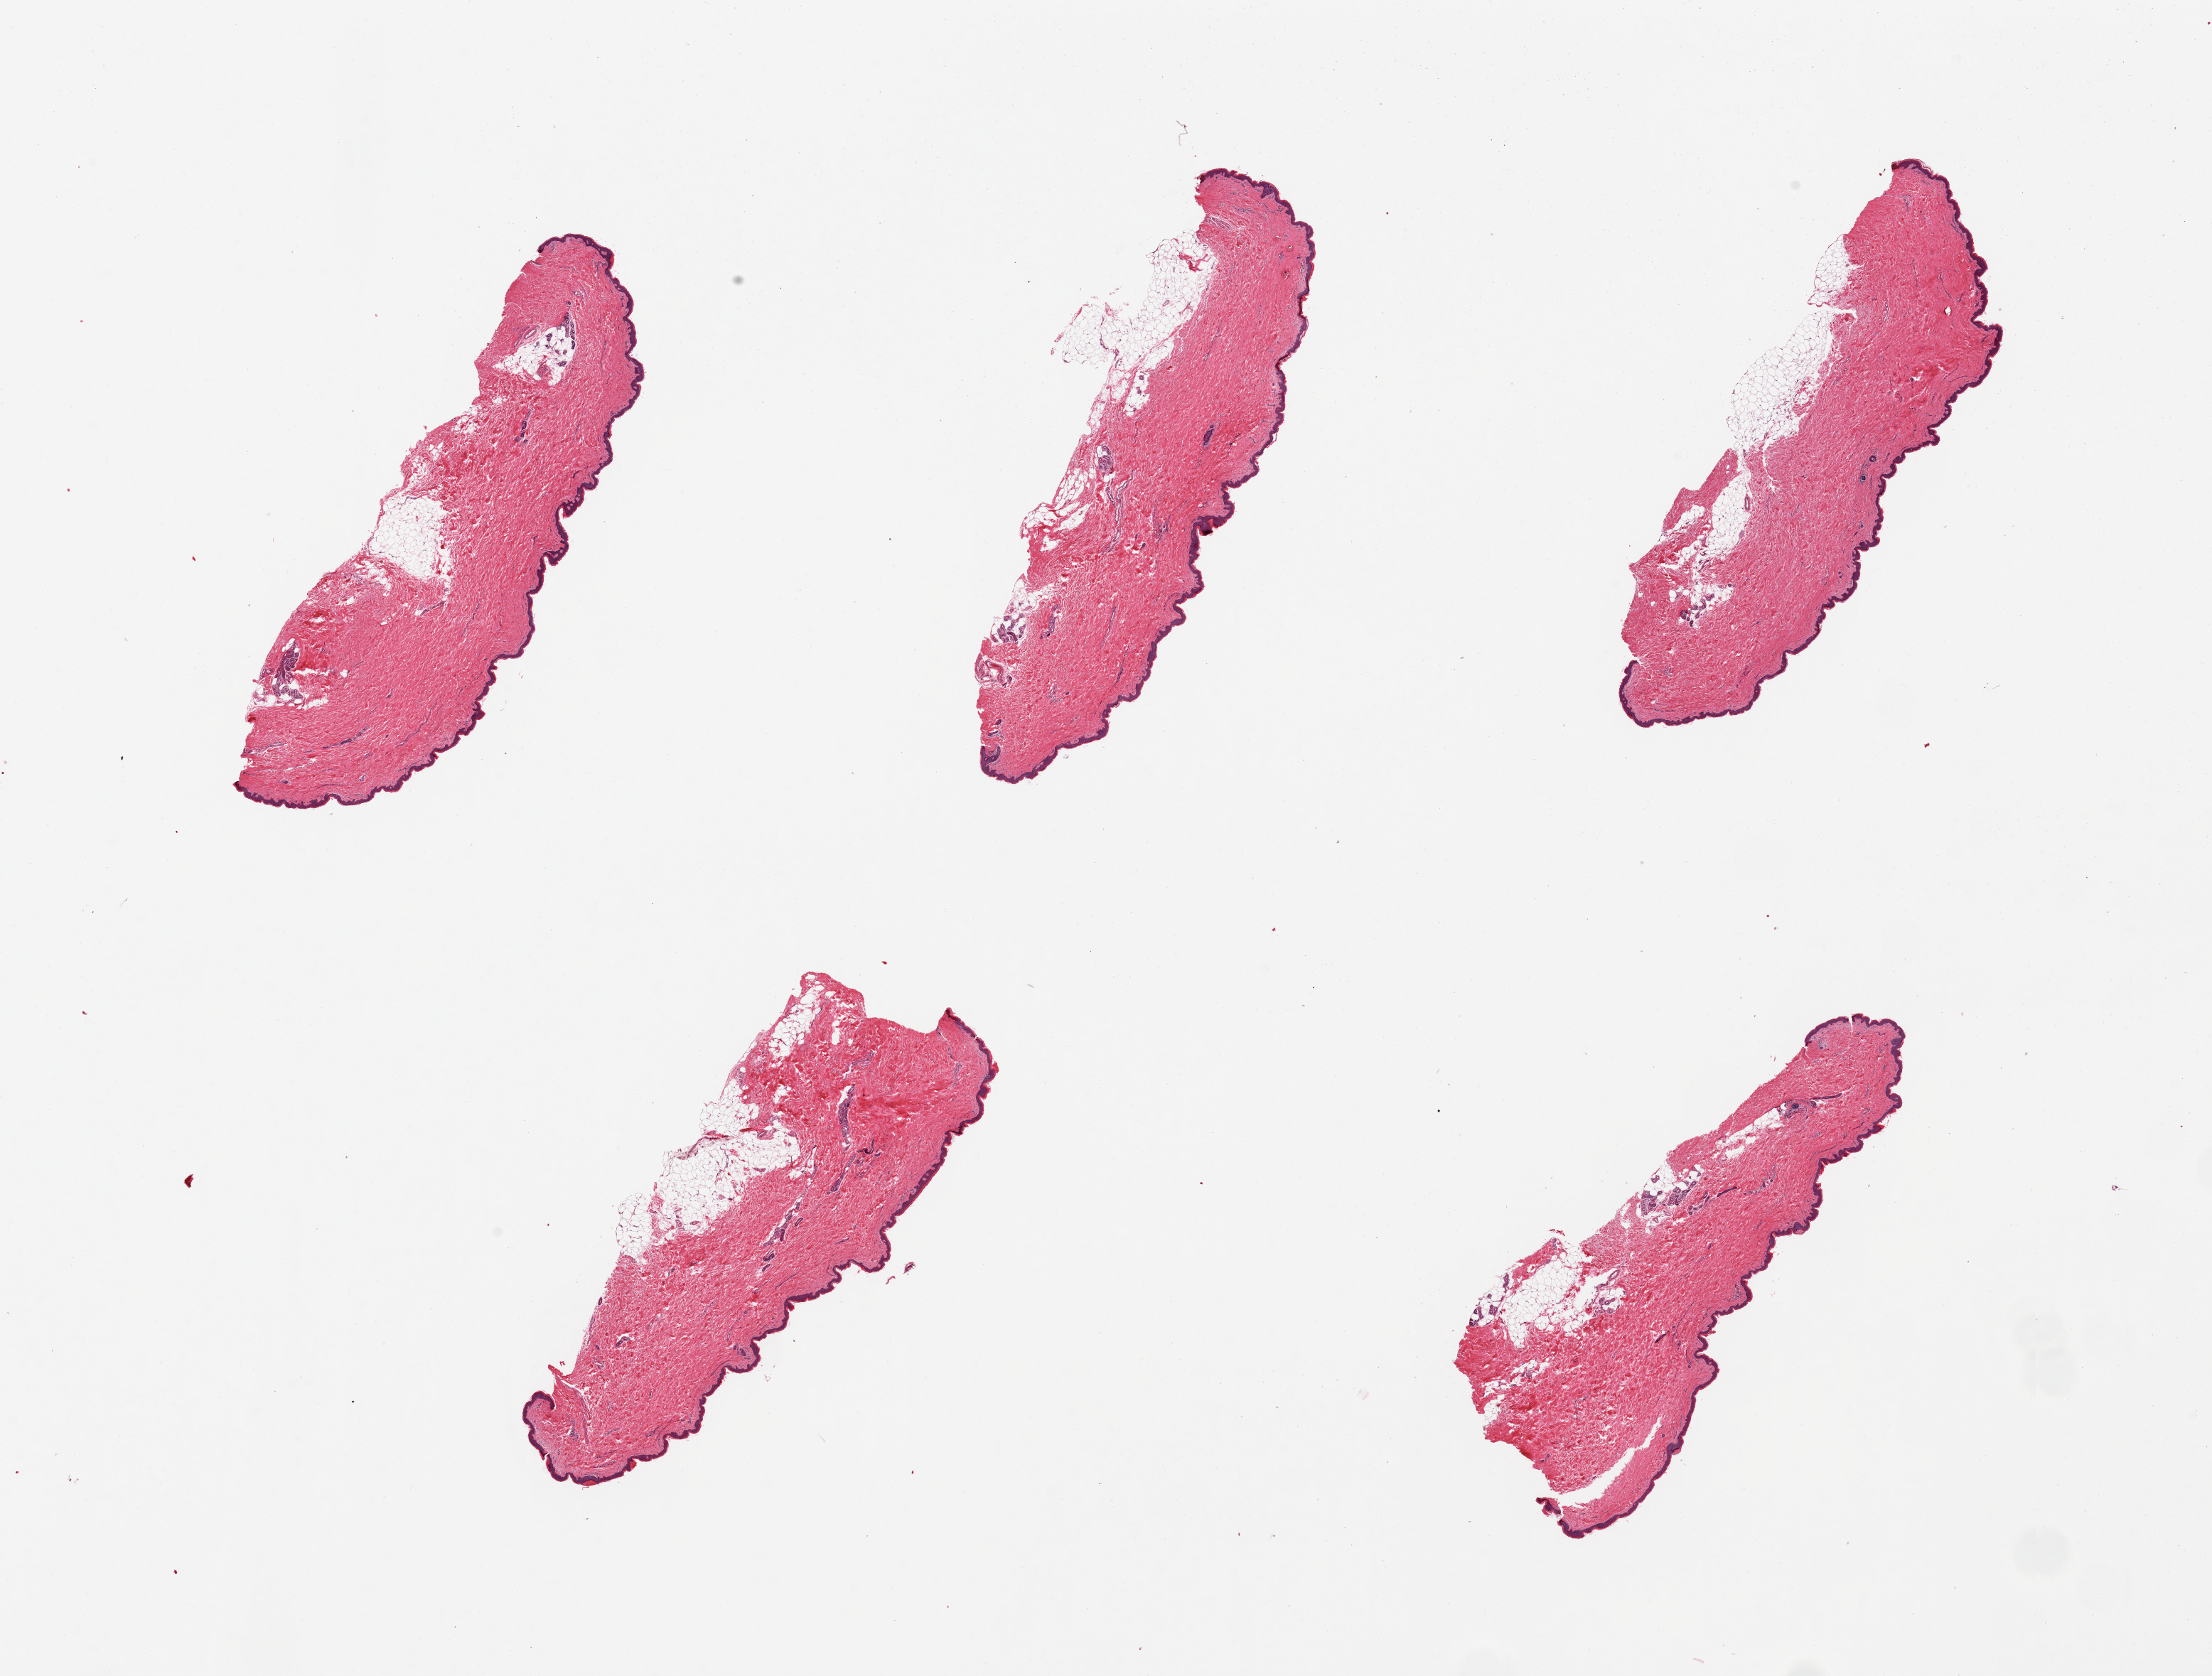
Whole-slide image, haematoxylin and eosin stain — a low-resolution overview of the entire scanned area, about 24.6 x 18.6 mm (from a 20x scan). PAXgene-fixed, paraffin-embedded tissue. Target tissue: skin of suprapubic region. Tissue donor sample. Donor sex: female.
• review note (as recorded): 6 pieces; squamous epithelium averages ~50 microns, 1-2% thickness, trace adherent fat